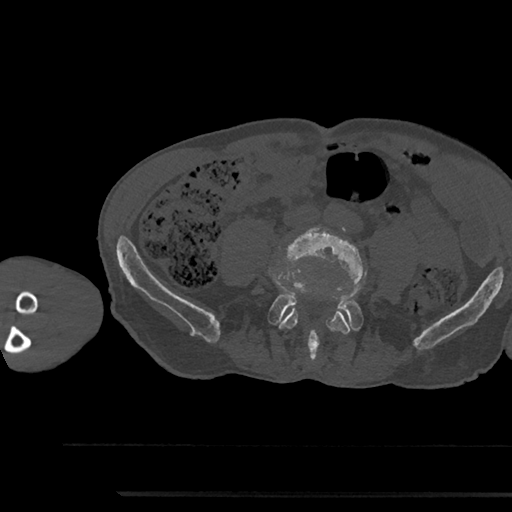
CT including the spine, one axial slice. Slice 378 of 797 in the series (ordered by position). Reconstruction kernel Br40s/3. 120 kVp. Bone window (W 1800 / L 400 HU). 0.5 mm slice thickness. 512 × 512 image matrix, field of view 367 × 367 mm. Patient: male, 79 years. Case-level facts recorded for this patient, not image findings: primary cancer: prostate.
Outlined on this slice (semi-automatic segmentation, software-assisted and operator-edited):
- L4 vertebra: bounding box [x1, y1, x2, y2] px = [278, 228, 364, 334]
- L5 vertebra: [239, 283, 362, 358]